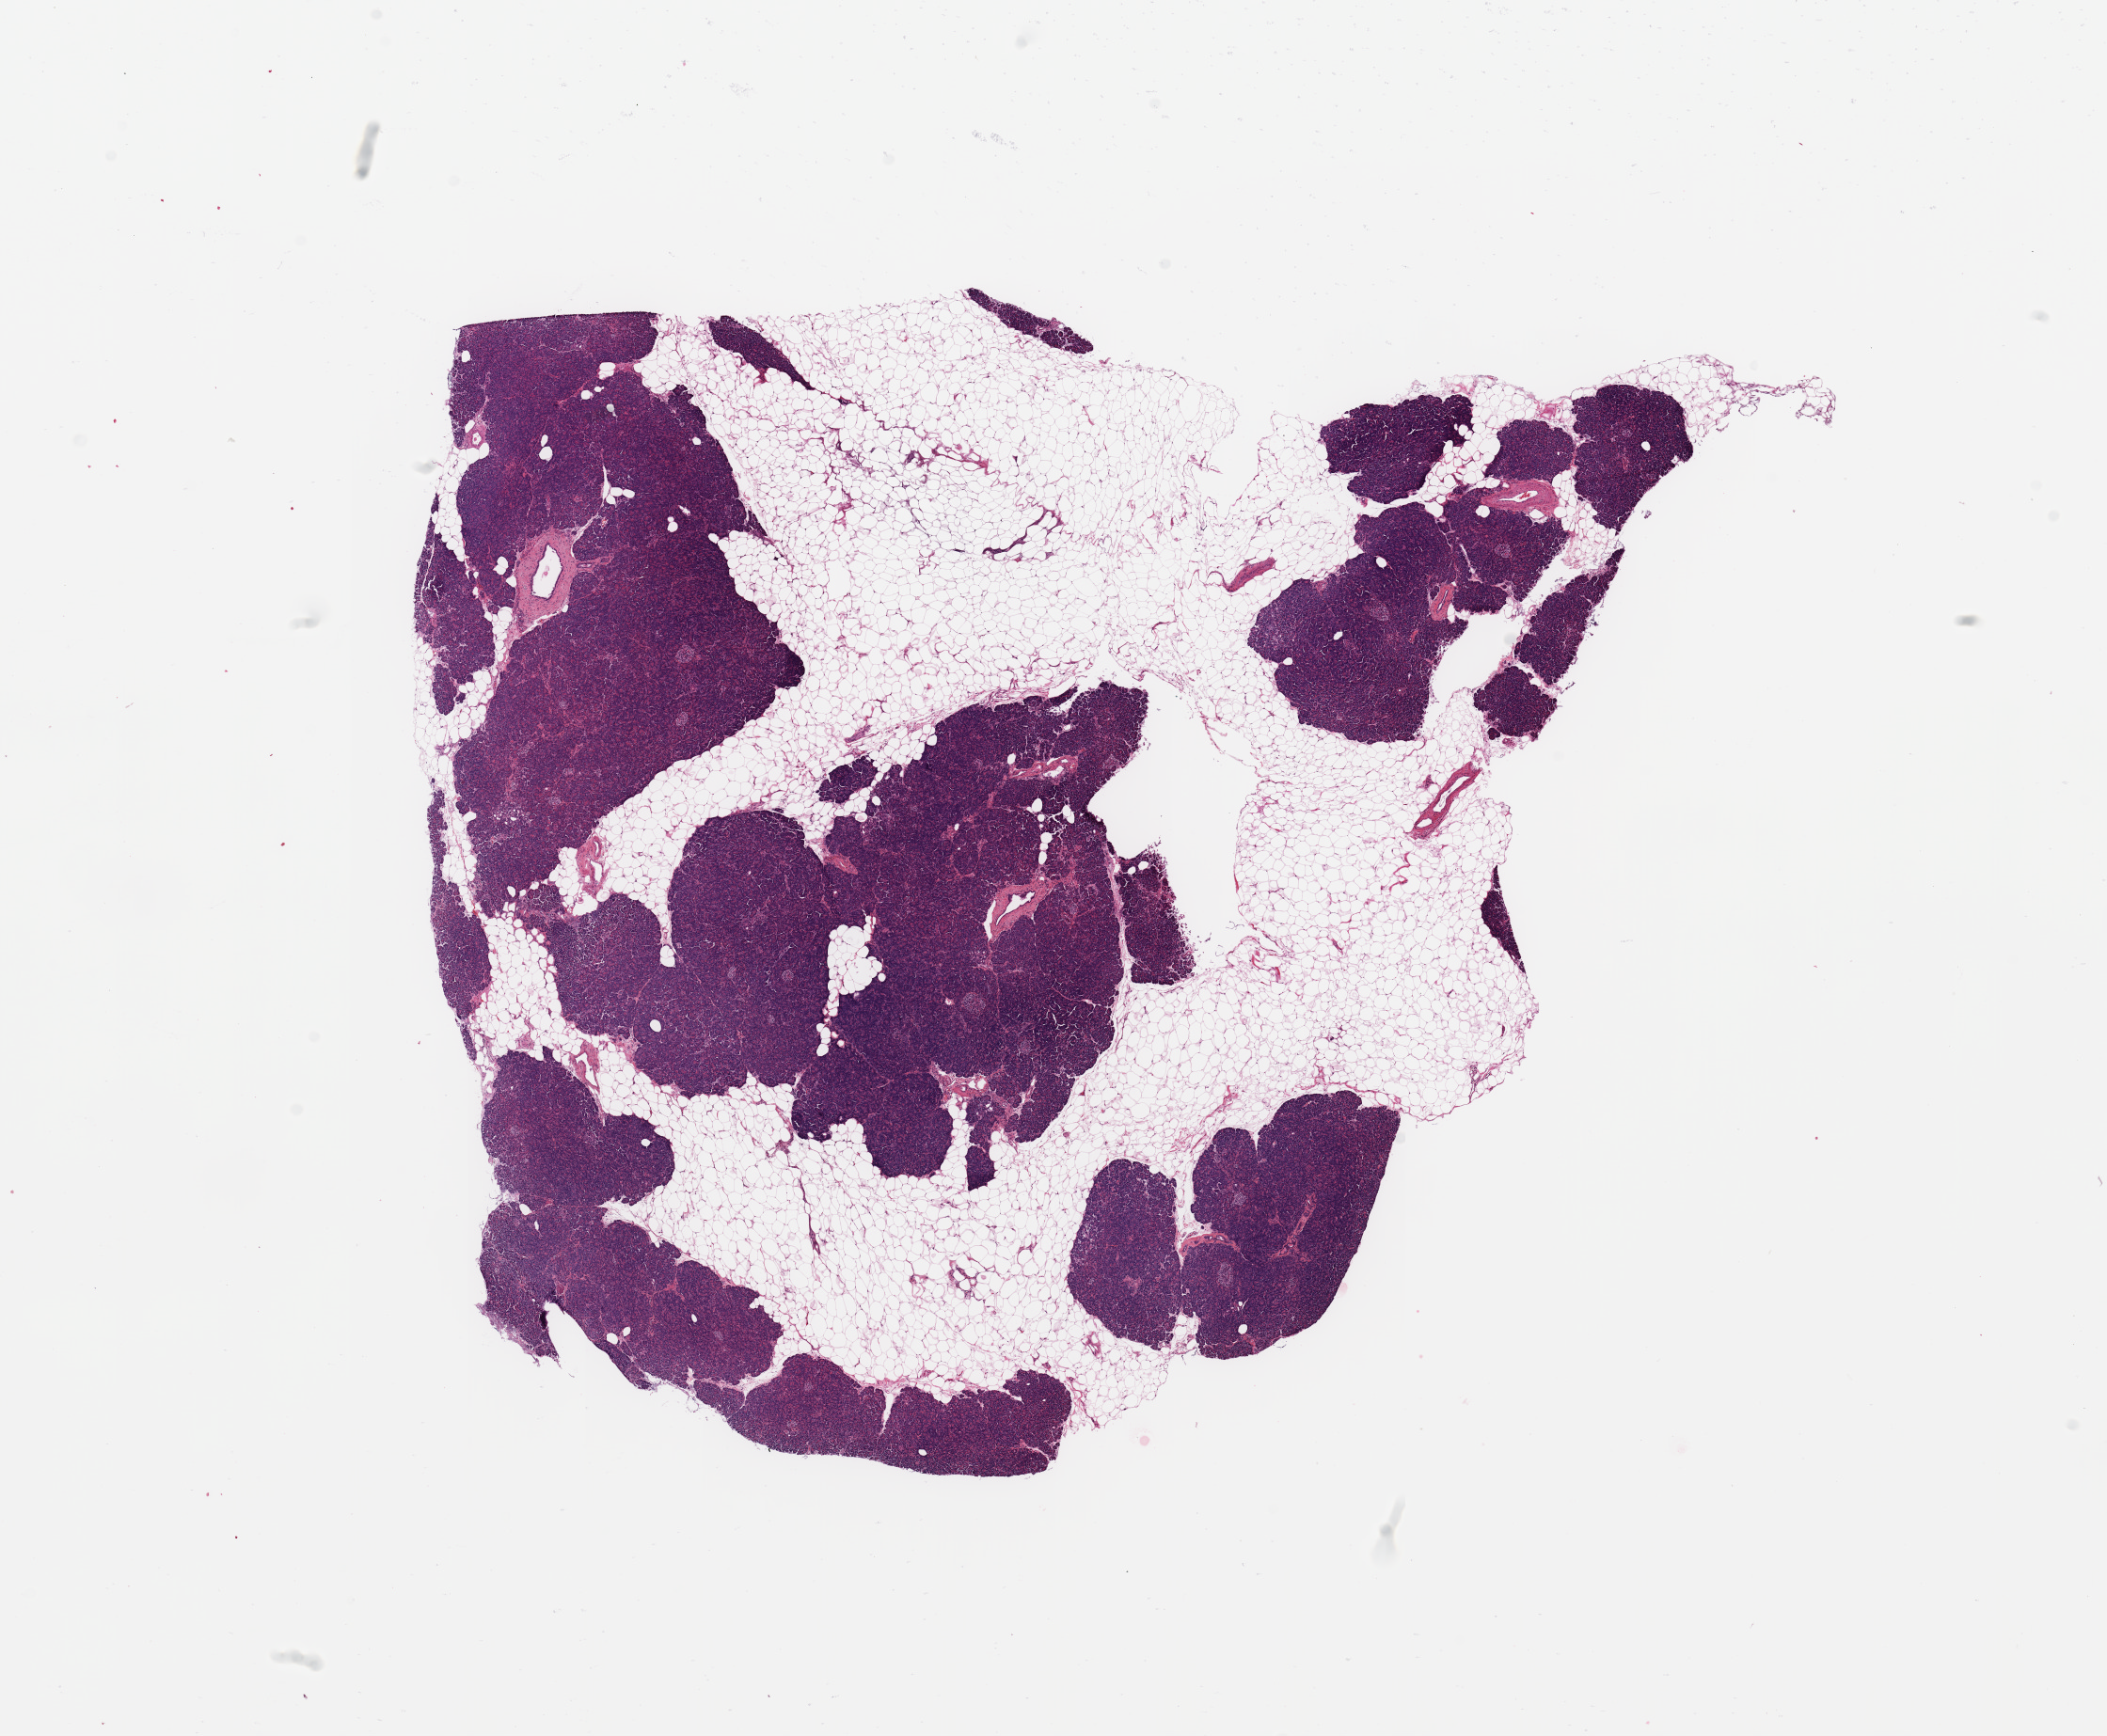
Whole-slide histology image, Hematoxylin and eosin (H&E) stained, shown as a low-resolution overview of the whole scanned area (about 17.7 x 14.6 mm). Normal (non-tumour) tissue sample, sampled site: pancreas. Patient: female, age 76 years.
This section: normal (non-tumour) tissue from the same patient. Patient diagnosis: Infiltrating duct carcinoma, NOS.